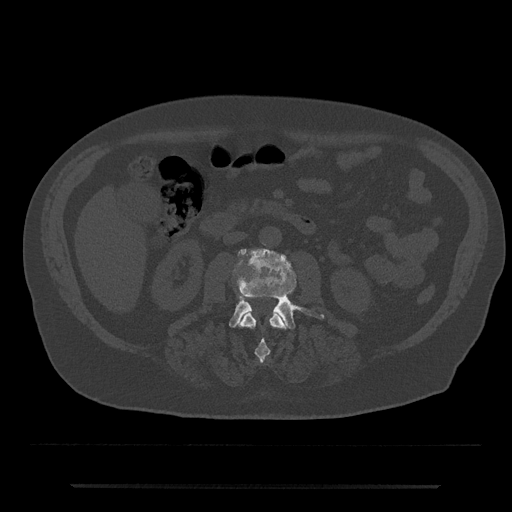
CT including the spine, one axial slice. Position 433 of 797 along the scan axis. Reconstruction kernel Br40s/3. Bone window (W 1800 / L 400 HU). 0.5 mm slice thickness. 512 × 512 image matrix, field of view 434 × 434 mm. Male patient, age 80 years. Case-level facts recorded for this patient, not image findings: primary cancer: prostate.
Outlined on this slice (semi-automatically segmented with operator editing):
- L2 vertebra: bounding box [x1, y1, x2, y2] px = [240, 310, 286, 362]
- L3 vertebra: [229, 248, 324, 329]